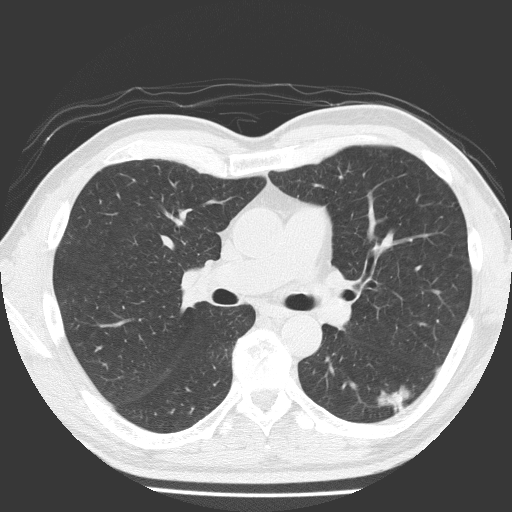
Low-dose screening chest CT, one axial slice; slice 108 of 184 in the series (ordered by position); reconstruction kernel FC51; 120 kVp; lung window (W 1500 / L -600 HU); 512 × 512 image matrix.
Annotated regions visible in this slice (manually delineated by an expert):
- lesion 1 (tumor, lower lobe of left lung): box from (x=378, y=386) to (x=410, y=415) px